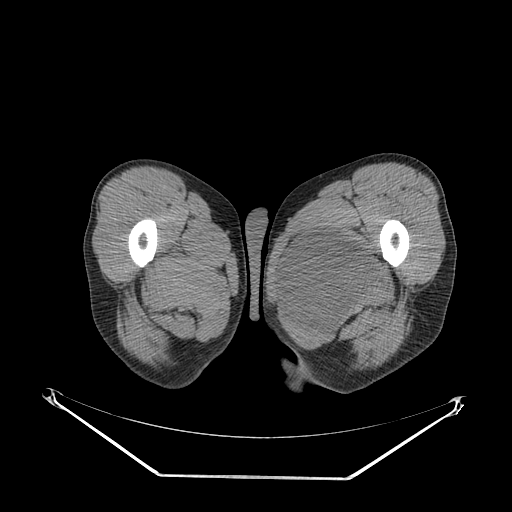
CT of an extremity soft-tissue mass (from a PET/CT study), one axial slice. Slice 32 of 267 in the series (ordered by position). Reconstruction kernel SOFT. 140 kVp. Soft-tissue window (W 400 / L 40 HU). 3.75 mm slice thickness. 512 × 512 image matrix, field of view 500 × 500 mm. Male patient. Case-level facts recorded for this patient, not image findings: histological type: pleiomorphic liposarcoma; grade: high; site of the primary tumour: left thigh.
Outlined on this slice (expert contour drawn on MRI and transferred to this co-registered scan by the dataset authors):
- gross tumour volume including surrounding oedema: box from (x=283, y=228) to (x=378, y=323) px
- gross tumour volume (mass): (x=285, y=230)–(x=376, y=316)